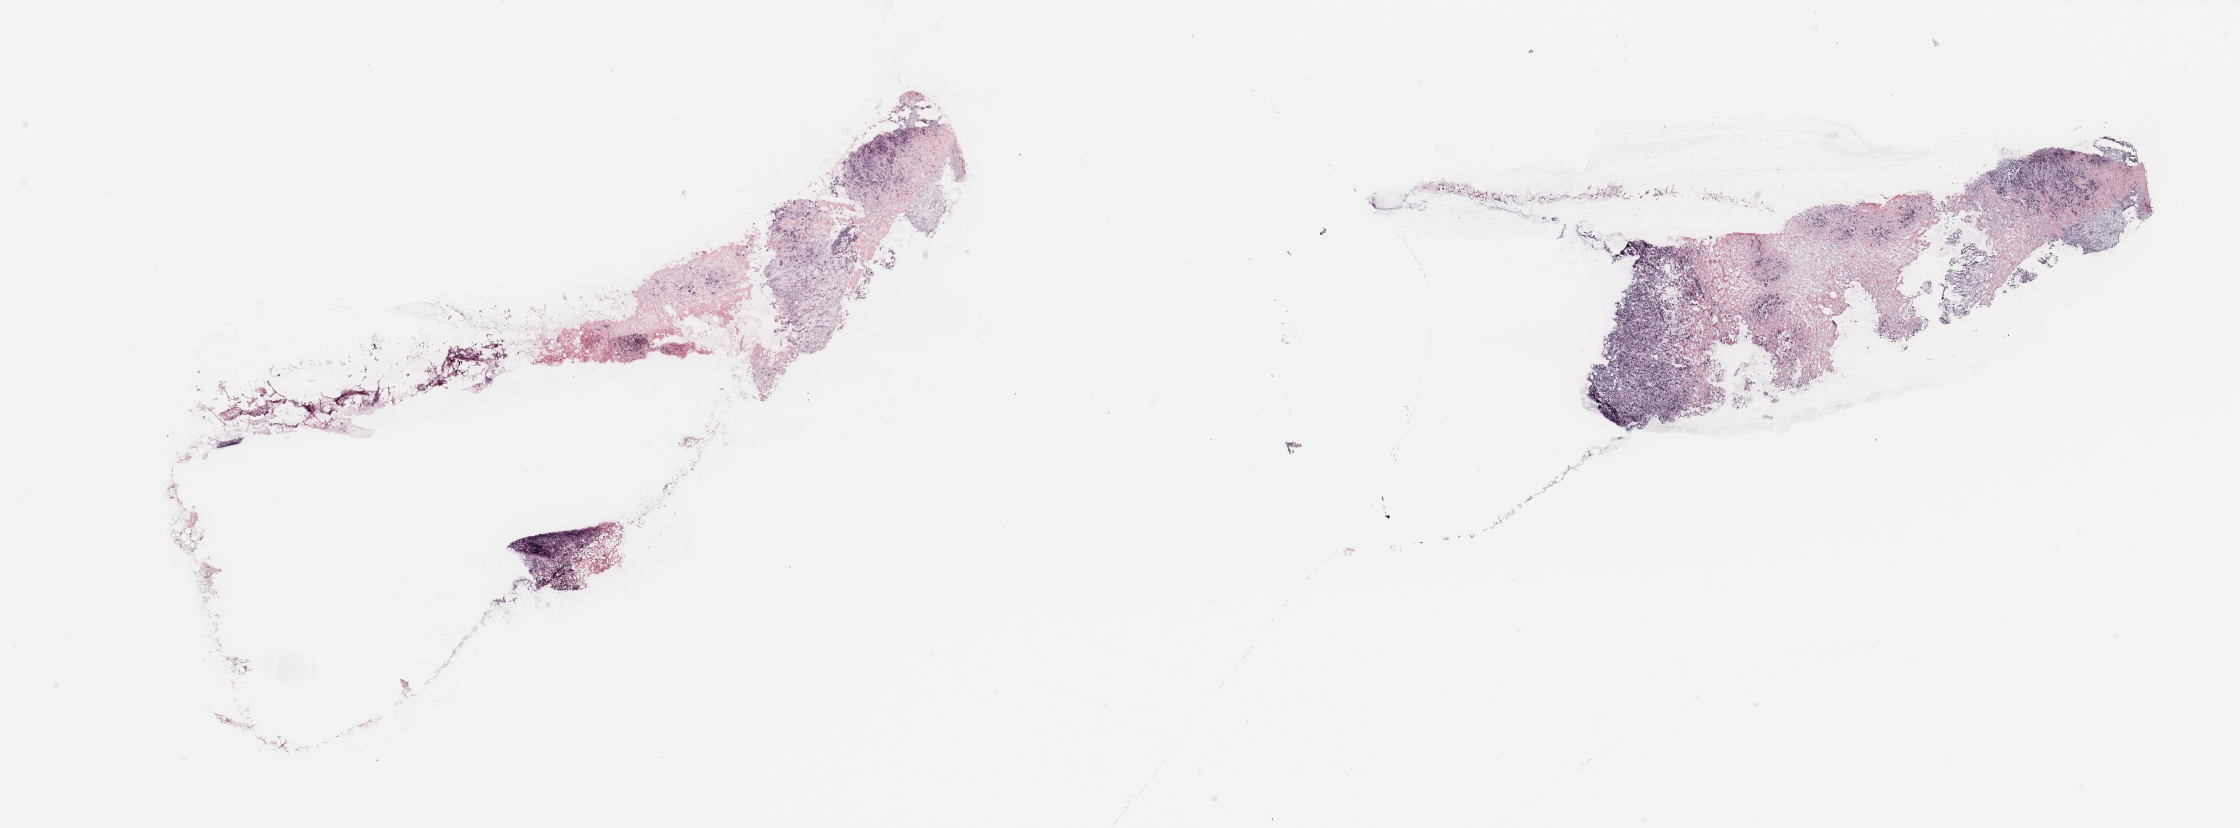
Hematoxylin and eosin (H&E) stained whole-slide image — low-resolution overview of the scanned area, about 35.4 x 13.1 mm (acquisition: 20x scan). Breast, tumour tissue. Patient: female, age 35 years.
Diagnosis: Infiltrating duct carcinoma, NOS.